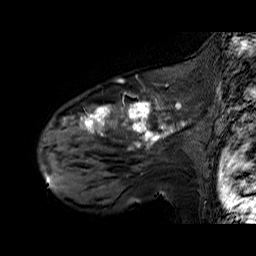
Breast MRI (dynamic contrast-enhanced), one sagittal slice; position 45 of 60 along the scan axis; dynamic contrast-enhanced series, time point 2 of 6 at this slice position (early post-contrast); 1.5 T; TE 6.3 ms, TR 32.9 ms; 4 mm slice thickness; 256 × 256 image matrix, field of view 200 × 200 mm. Female patient. Case-level facts recorded for this patient, not image findings: setting: breast cancer imaged before/during neoadjuvant chemotherapy; receptor status: HER2-positive.
Outlined on this slice (semi-automatically segmented with operator editing):
- analysis volume of interest (the breast-tissue region the enhancement analysis was run in; not a lesion): bounding box [x1, y1, x2, y2] px = [48, 92, 195, 174]
- tumour enhancement mask (voxels above the 100 % enhancement threshold inside the analysis volume of interest): [63, 101, 185, 150]